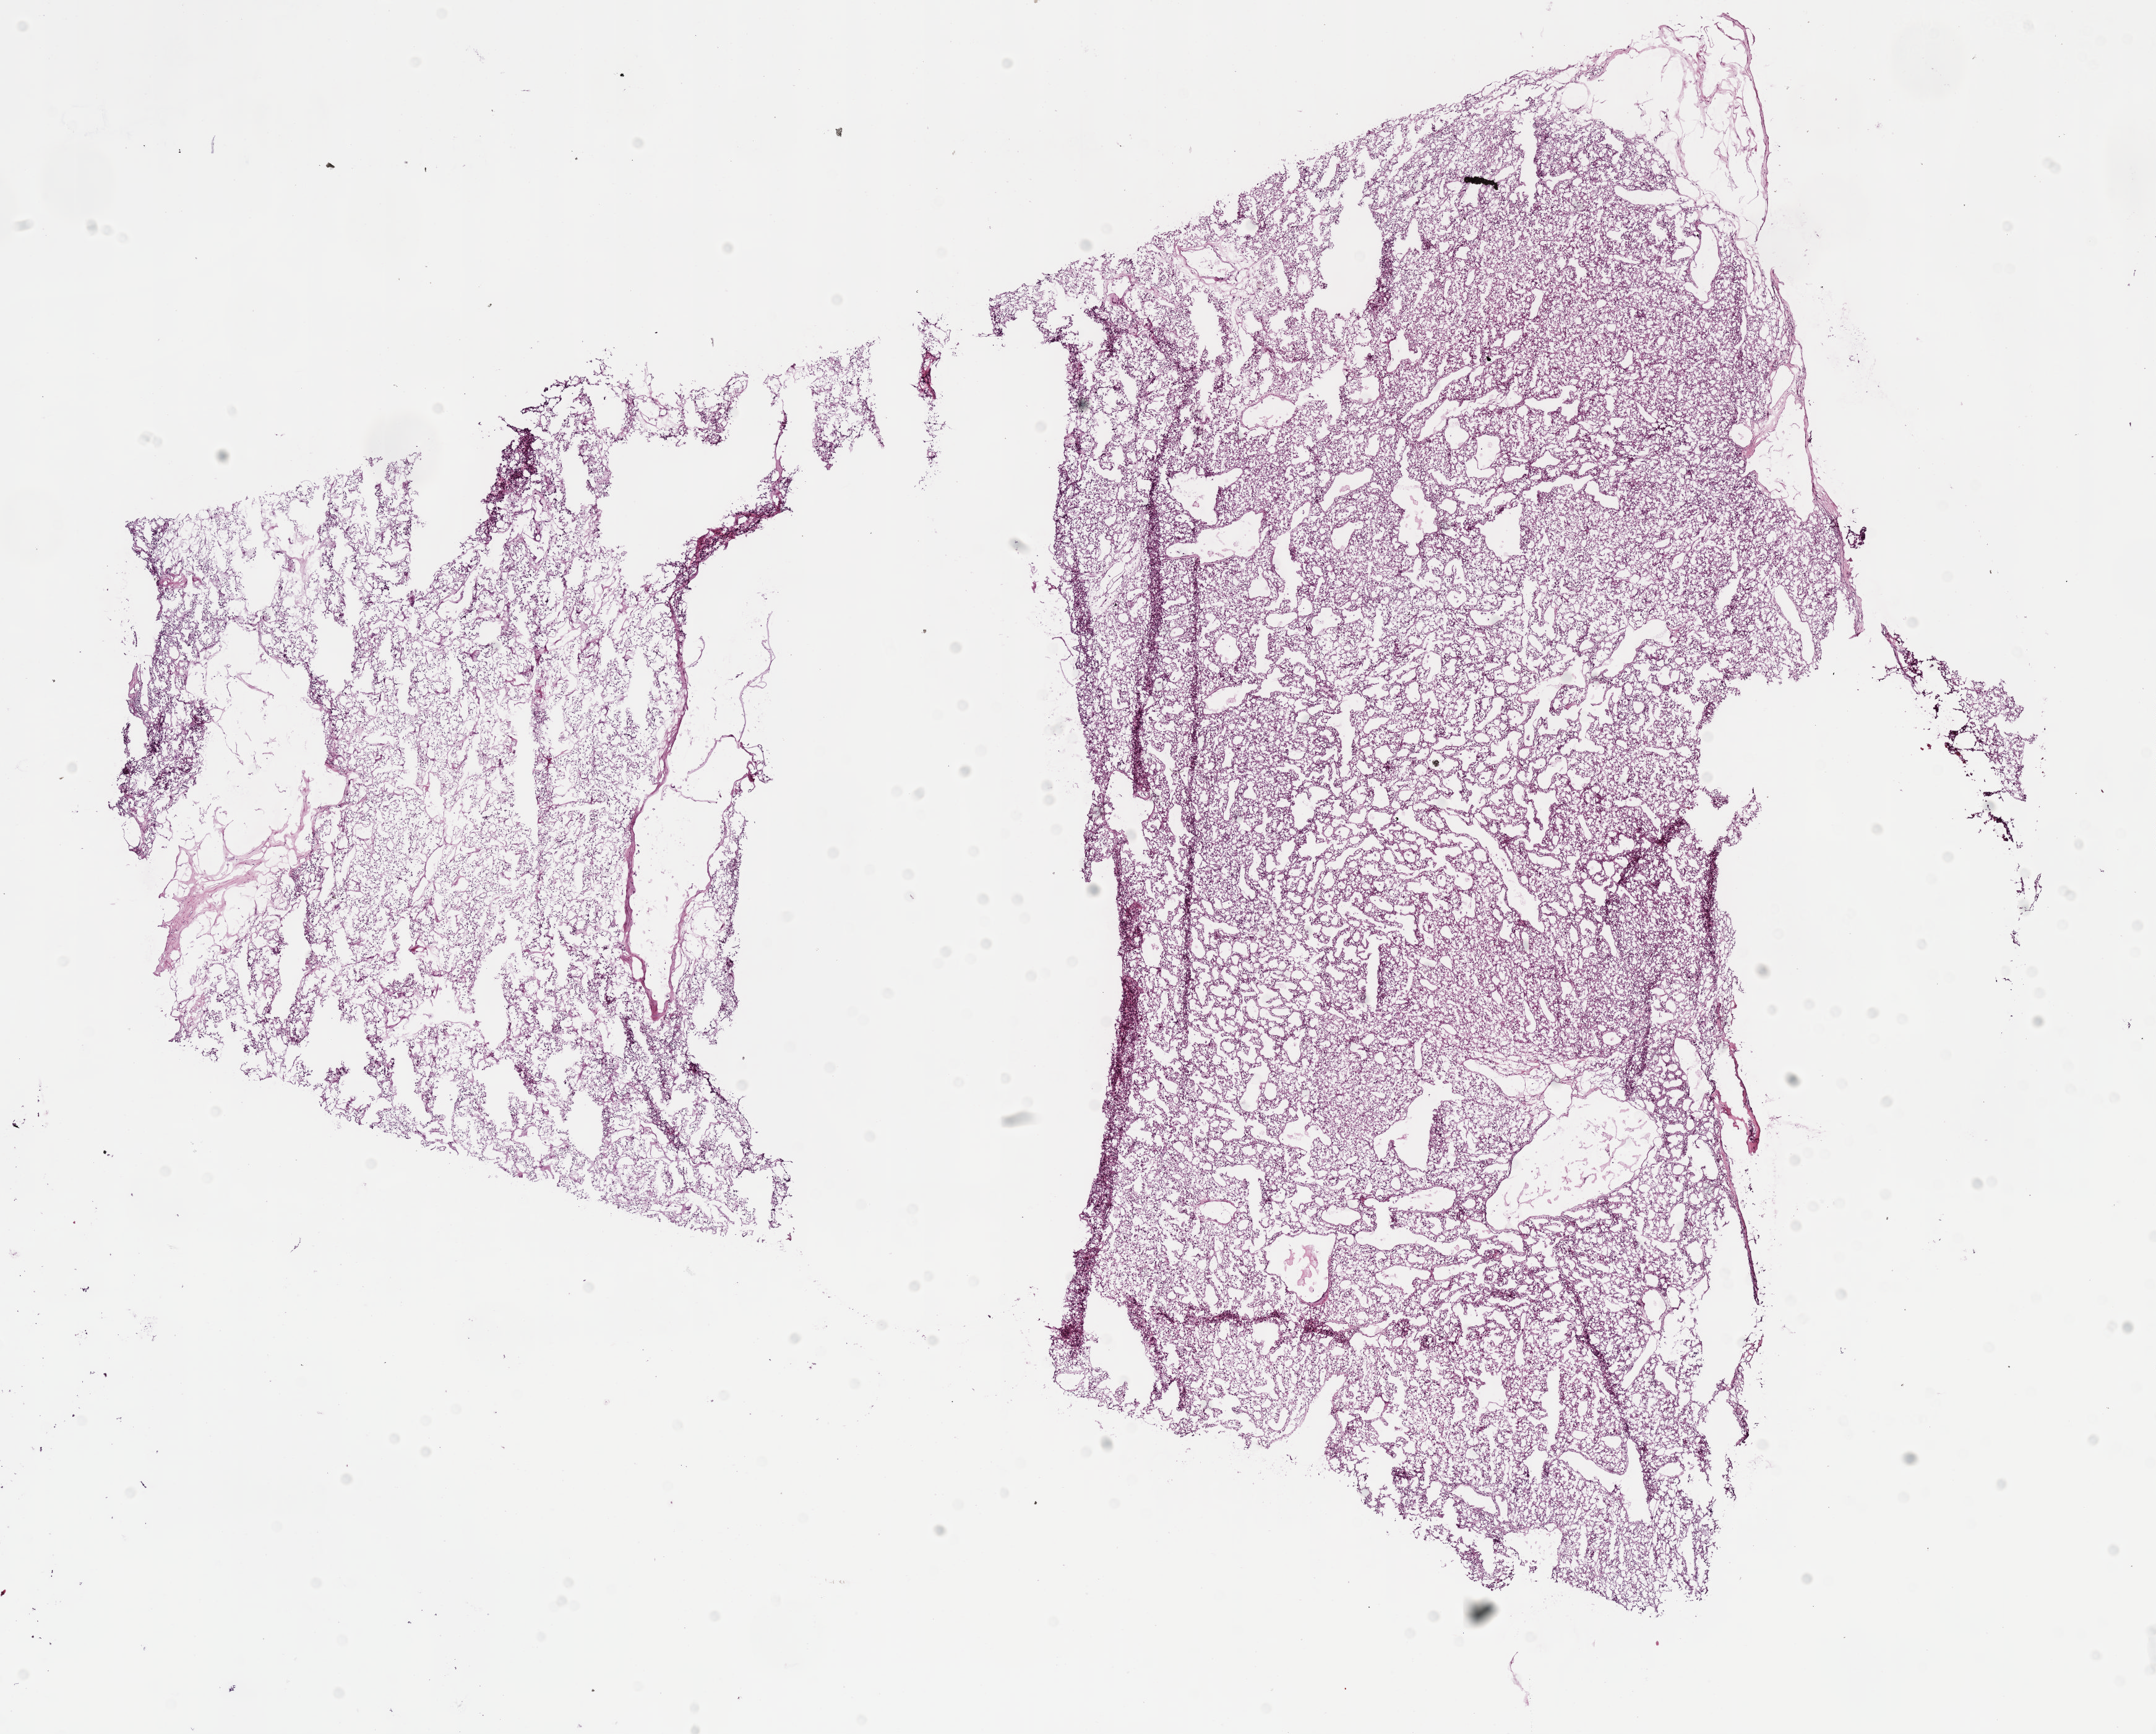
Digitized Hematoxylin and eosin (H&E) stained tissue section (whole slide), low-resolution overview of the scanned area, about 14.1 x 11.3 mm. Frozen section from the bottom of the tissue portion. Primary tumour sample from the kidney. Male, age 57 years at initial diagnosis. Histologic grade: G2 (moderately differentiated). Slide review estimates, as recorded: tumour cells 95%, tumour nuclei 85%, normal cells 0%, stromal cells 5%, necrosis 0%.
• TNM: T3a NX M0
• AJCC pathologic stage: III
• pathologic diagnosis: Clear cell adenocarcinoma, NOS